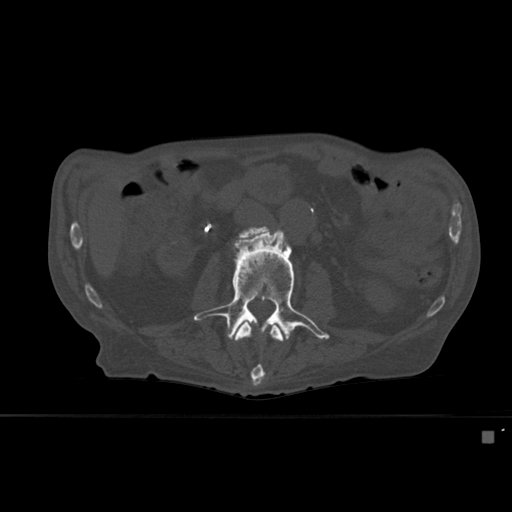
CT including the spine, one axial slice. Position 217 of 527 along the scan axis. Bone window (W 1800 / L 400 HU). 512 × 512 image matrix, field of view 373 × 373 mm. Male patient, age 78 years. Case-level facts recorded for this patient, not image findings: primary cancer: prostate.
Structures marked on this image (semi-automatically segmented with operator editing):
- L2 vertebra: box from (x=231, y=320) to (x=283, y=386) px
- L3 vertebra: (x=193, y=227)–(x=330, y=341)
- L4 vertebra: (x=240, y=227)–(x=266, y=238)